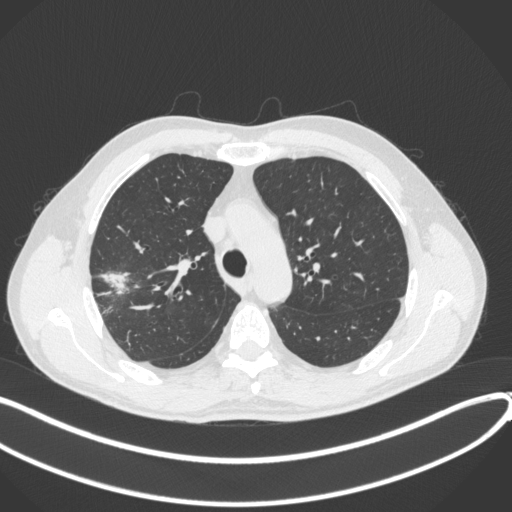
Chest CT, one axial slice. Slice 304 of 381 in the series (ordered by position). Reconstruction kernel B31f. 120 kVp. Lung window (W 1500 / L -600 HU). 1 mm slice thickness. 512 × 512 image matrix, field of view 400 × 400 mm. Male patient, age 62 years. Case-level facts recorded for this patient, not image findings: clinical TNM (as recorded): T1c N0 M0.
Structures marked on this image (bounding box drawn by a radiologist):
- lung tumour (recorded histology: adenocarcinoma): box from (x=95, y=261) to (x=134, y=299) px